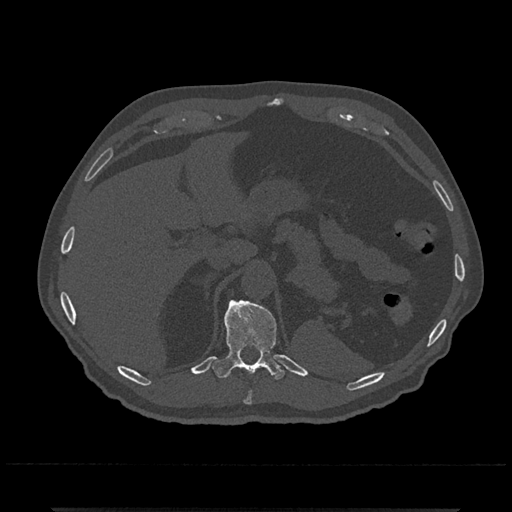
CT including the spine, one axial slice; slice 503 of 797 in the series (ordered by position); reconstruction kernel Br40s/3; bone window (W 1800 / L 400 HU); 512 × 512 image matrix, field of view 393 × 393 mm. Male patient, age 67 years. From the clinical record (not read from this slice): primary cancer: prostate.
Outlined on this slice (semi-automatic segmentation, software-assisted and operator-edited):
- T10 vertebra: box from (x=244, y=390) to (x=252, y=404) px
- T11 vertebra: (x=212, y=299)–(x=285, y=380)